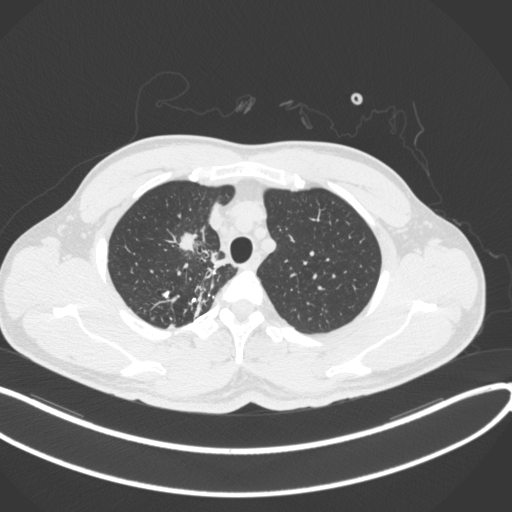
Chest CT, one axial slice. Position 305 of 391 along the scan axis. Lung window (W 1500 / L -600 HU). 1 mm slice thickness. 512 × 512 image matrix, field of view 400 × 400 mm. Patient: male, 48 years. Case-level facts recorded for this patient, not image findings: clinical TNM (as recorded): T1c N1 M1.
Annotated regions visible in this slice (rectangle marked by the reading radiologist):
- lung tumour (recorded histology: adenocarcinoma): bounding box [x1, y1, x2, y2] px = [176, 228, 207, 257]